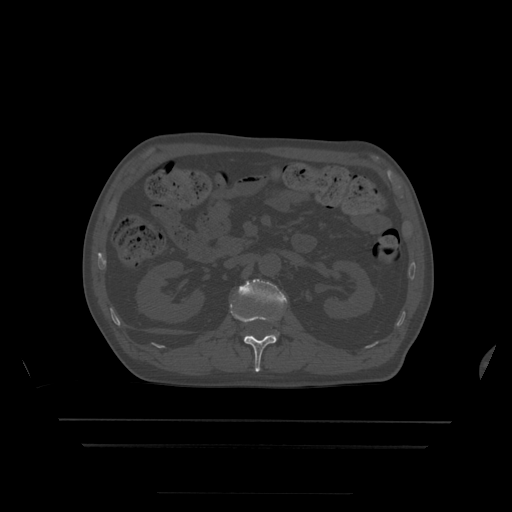
CT including the spine, one axial slice. Position 161 of 522 along the scan axis. Bone window (W 1800 / L 400 HU). 512 × 512 image matrix, field of view 436 × 436 mm. Patient age 68 years. From the clinical record (not read from this slice): primary cancer: urothelial.
Structures marked on this image (semi-automatically segmented with operator editing):
- L1 vertebra: bounding box <230,304,277,372> (left, top, right, bottom; pixels)
- L2 vertebra: <239,279,287,309>